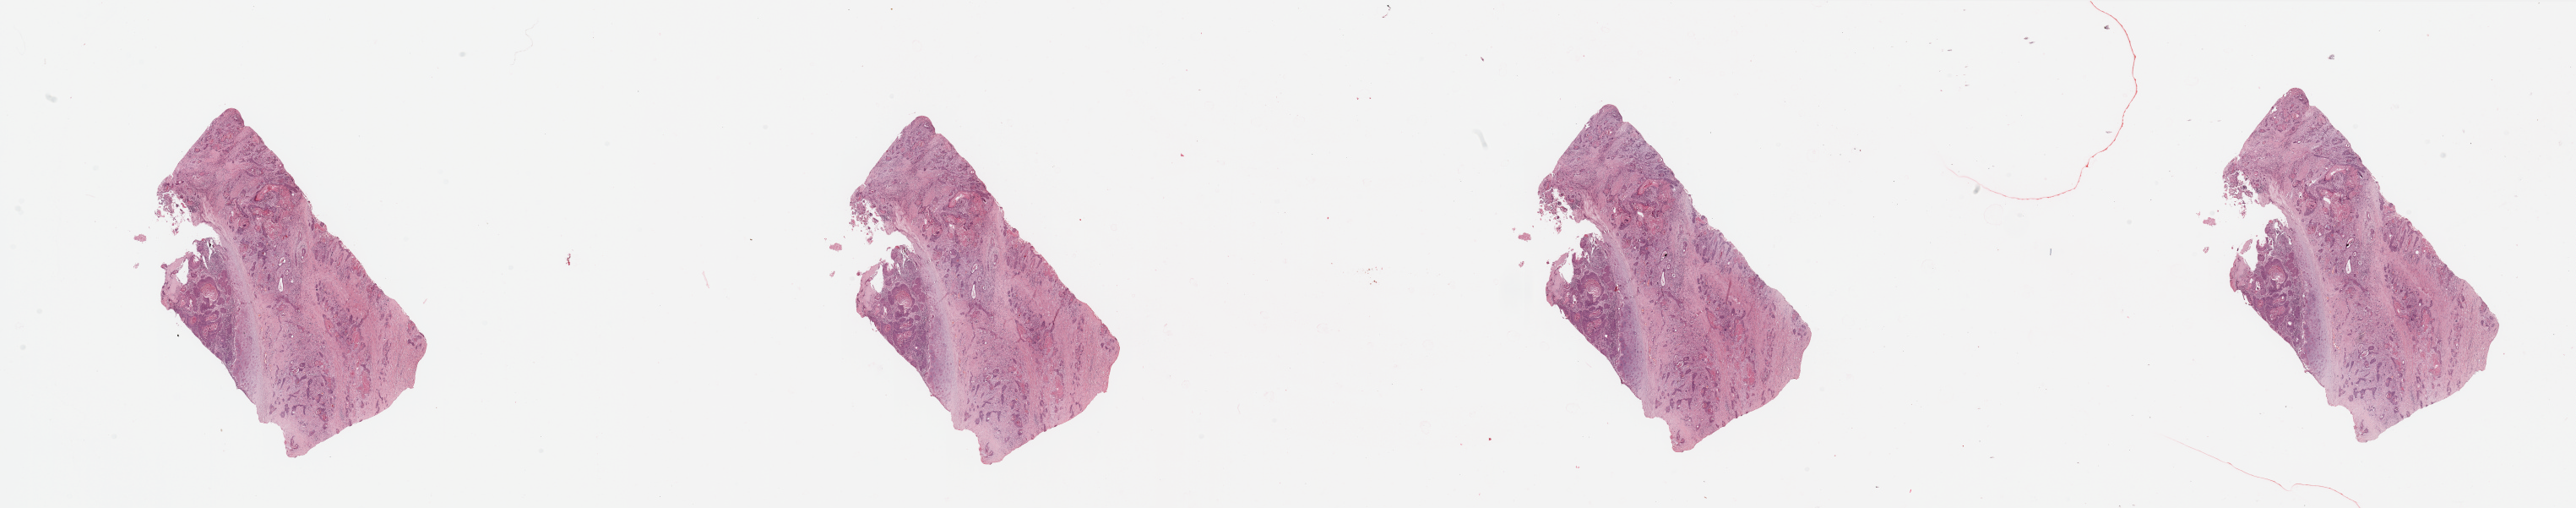
Digitized H&E-stained tissue section (whole slide) — a low-resolution overview of the entire scanned area, about 48.2 x 9.5 mm (from a 20x scan). Head and neck, tissue type not recorded. Patient: male, age 81 years.
- patient diagnosis: Squamous cell carcinoma, NOS (larynx, NOS)